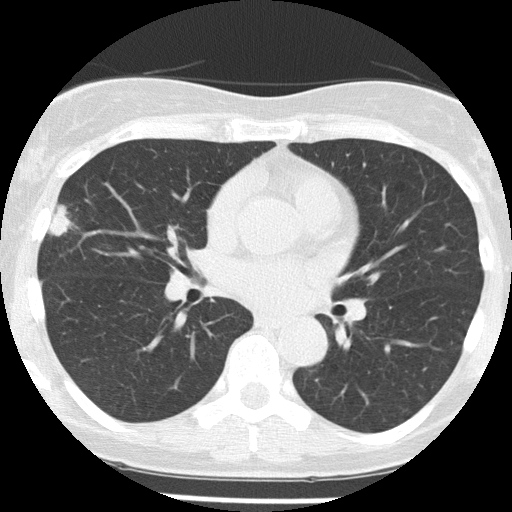
Low-dose screening chest CT, one axial slice; slice 84 of 156 in the series (ordered by position); reconstruction kernel FC51; 120 kVp; lung window (W 1500 / L -600 HU); 2 mm slice thickness; 512 × 512 image matrix, field of view 280 × 280 mm.
Annotated regions visible in this slice (expert manual segmentation):
- lesion 1 (tumor, middle lobe of right lung): bounding box <50,204,69,237> (left, top, right, bottom; pixels)